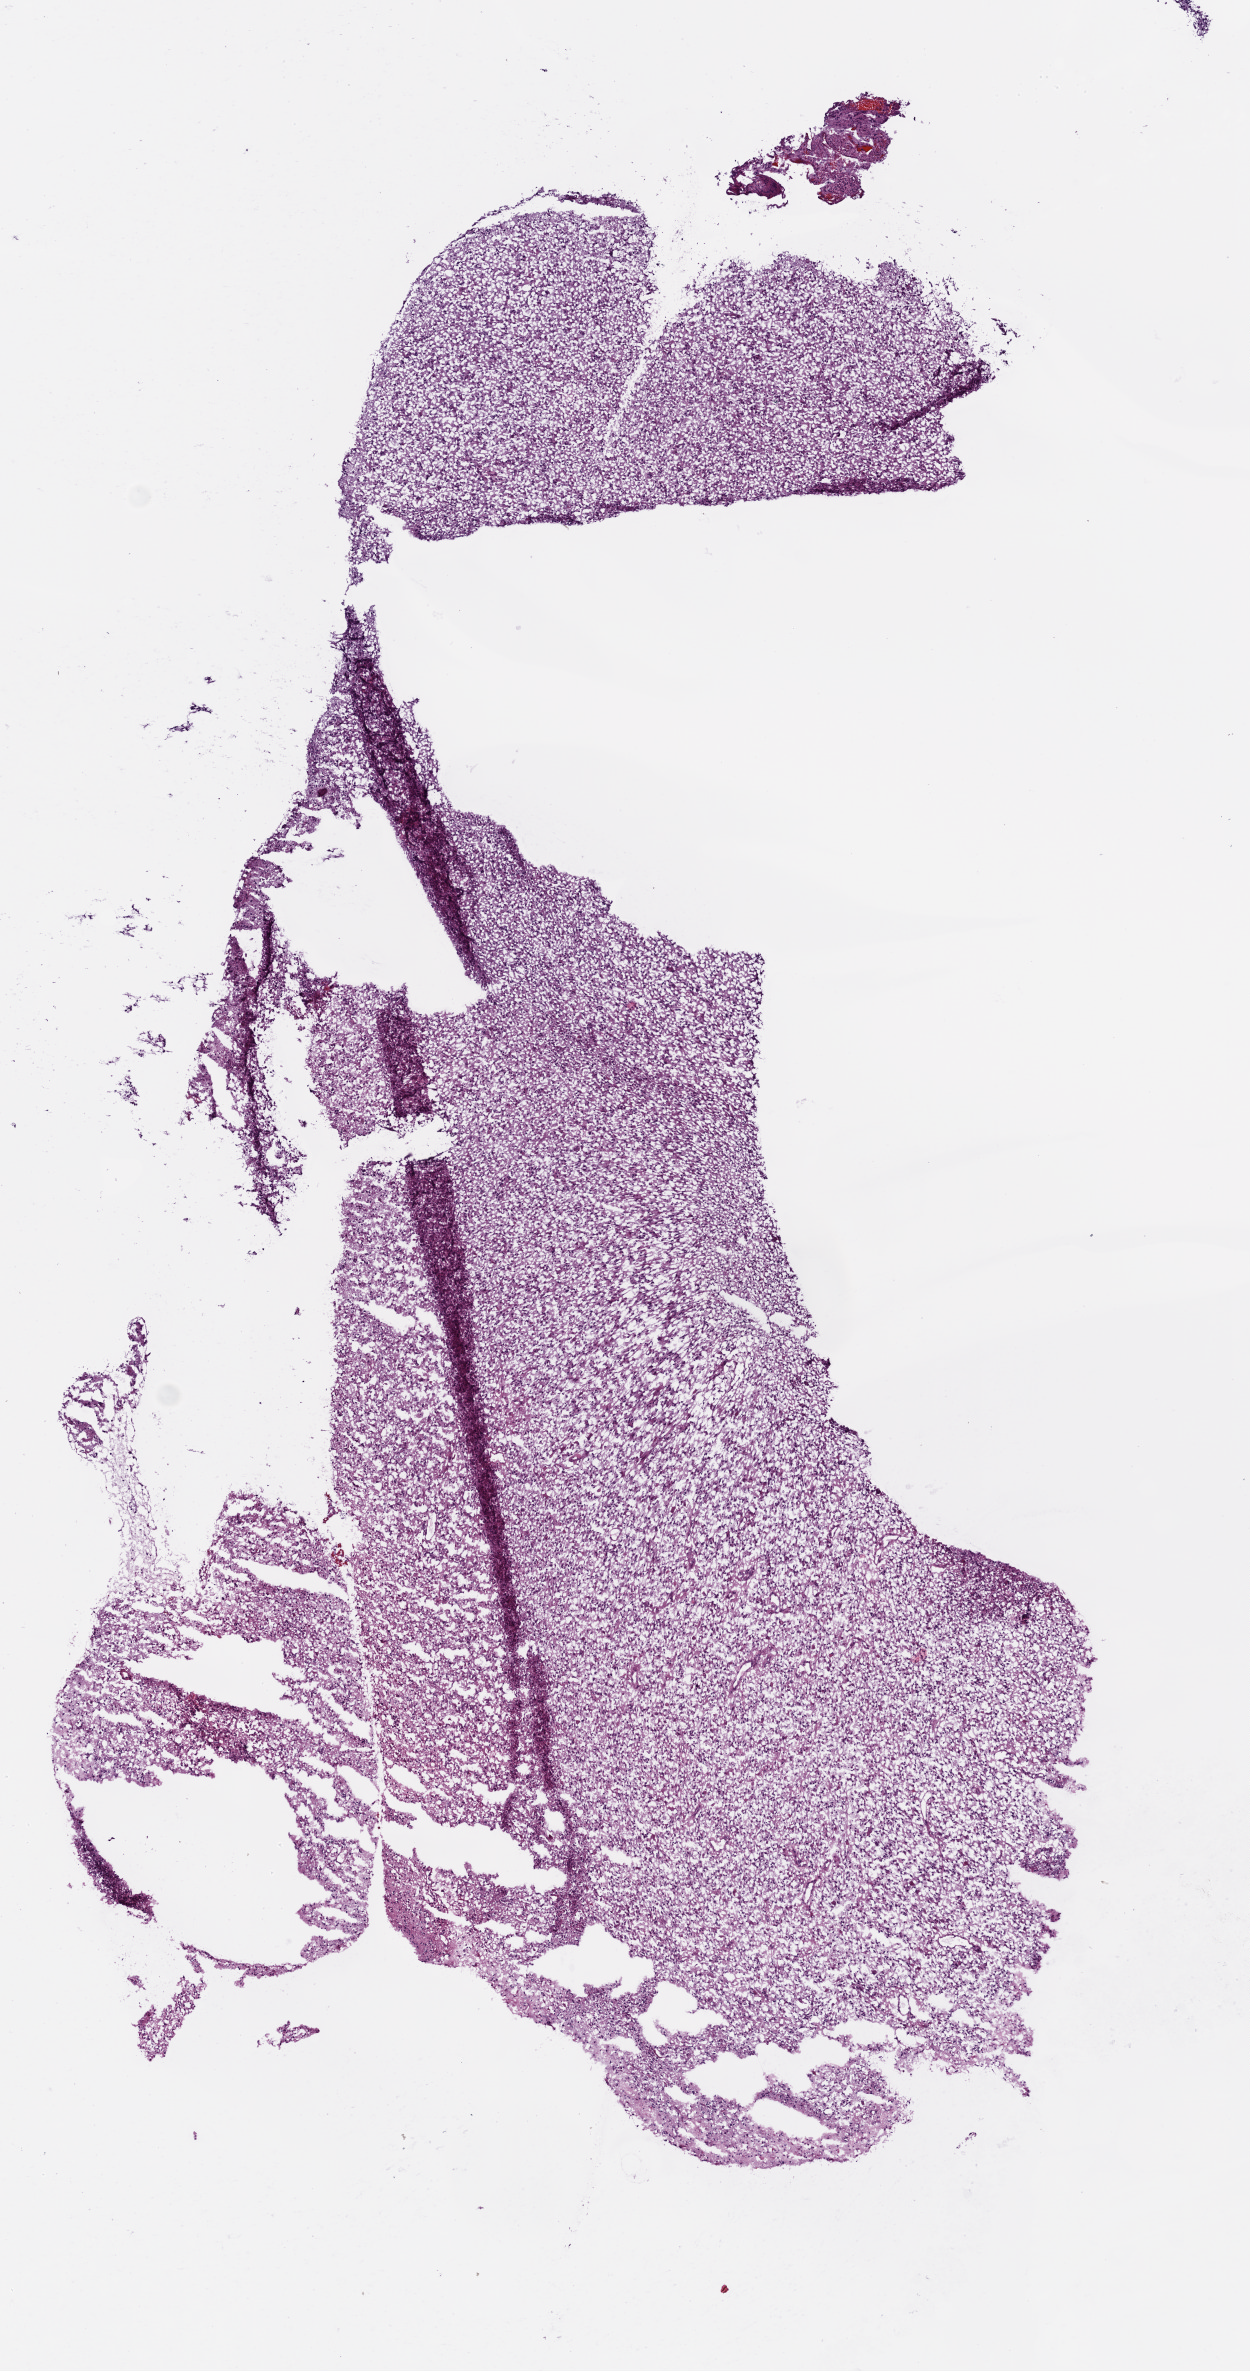
H&E whole-slide image, a low-resolution overview of the entire scanned area, about 5.0 x 9.5 mm, frozen section from the bottom of the tissue portion, primary tumour sample from the brain. Patient: male, age at initial diagnosis 36 years. Slide review estimates, as recorded: tumour cells 90%, tumour nuclei 90%, normal cells 0%, stromal cells 5%, necrosis 5%.
Diagnosis: Glioblastoma.